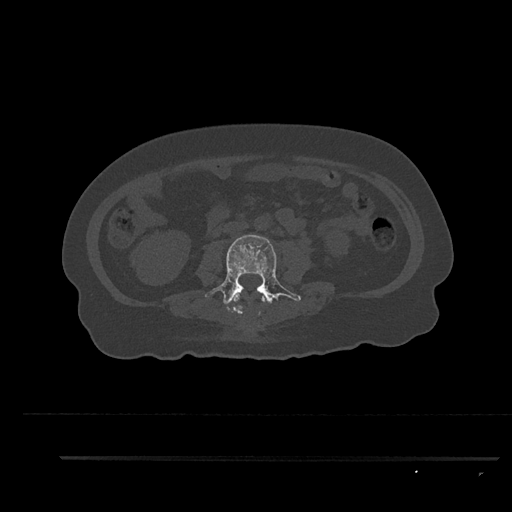
CT including the spine, one axial slice. Position 99 of 797 along the scan axis. Reconstruction kernel Br40s/3. 120 kVp. Bone window (W 1800 / L 400 HU). 0.5 mm slice thickness. 512 × 512 image matrix, field of view 408 × 408 mm. Patient: female, 44 years. Case-level facts recorded for this patient, not image findings: primary cancer: renal; vertebrae with lytic lesions (as recorded): L1.
Structures marked on this image (semi-automatically segmented with operator editing):
- L2 vertebra: bounding box (x1, y1, x2, y2) in pixels: (231, 294, 265, 315)
- L3 vertebra: (205, 235, 301, 313)